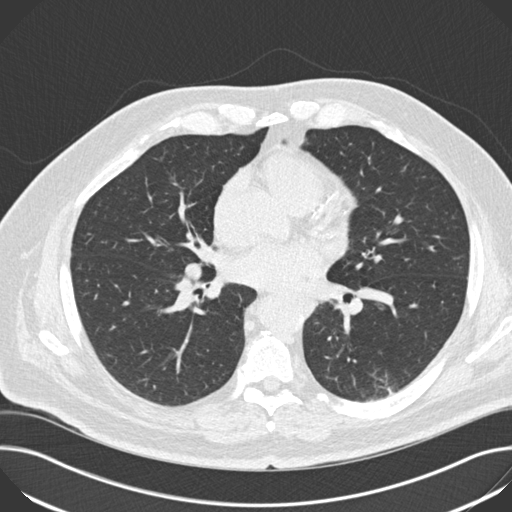
Chest CT (low-dose screening protocol), one axial image, third screening round (two years after baseline), lung window (W 1500 / L -600 HU), 2 mm slice thickness, slice 84 of 172 in the series. Male, age 68 years at enrolment. Current smoker at enrolment.
Lesion marked by an expert reader, bounding box <162,234,231,305> (left, top, right, bottom; pixels). No non-calcified nodule or mass ≥4 mm was recorded by the screening reader at this exam. Lung cancer was diagnosed 151 days after this screen: small cell carcinoma, NOS, right hilum, mediastinum, stage IV (AJCC 6th edition).